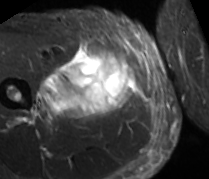
MRI of an extremity soft-tissue mass, one axial slice; position 32 of 89 along the scan axis; STIR; MR volume resampled by the dataset authors to the PET/CT grid (not the native acquisition matrix); 209 × 179 image matrix, field of view 204 × 175 mm. Male patient. Case-level facts recorded for this patient, not image findings: histological type: undifferentiated - pleiomorphic; grade: high; site of the primary tumour: right thigh.
Structures marked on this image (expert contour drawn on MRI and transferred to this co-registered scan by the dataset authors):
- gross tumour volume including surrounding oedema: bounding box [x1, y1, x2, y2] px = [30, 48, 134, 122]
- gross tumour volume (mass): [64, 53, 134, 118]